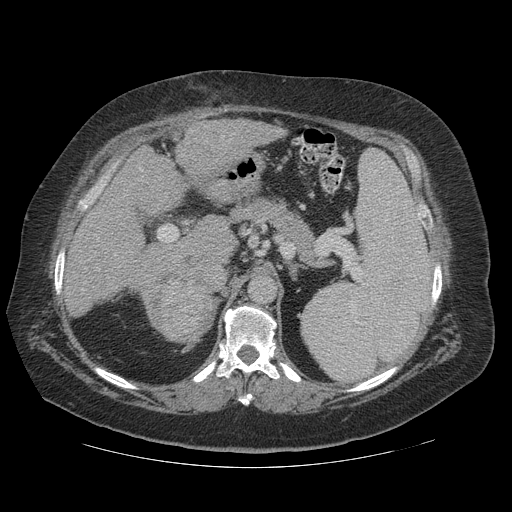
Contrast-enhanced abdominal CT (liver protocol), one axial slice. Slice 70 of 121 in the series (ordered by position). Soft-tissue window (W 400 / L 40 HU). 2.5 mm slice thickness. 512 × 512 image matrix, field of view 420 × 420 mm. From the clinical record (not read from this slice): diagnosis: hepatocellular carcinoma (patient treated with transarterial chemoembolisation; whether this scan precedes or follows treatment is not stated here); TNM stage (as recorded): Stage-IIIA; Child-Pugh class: A; tumour nodularity: multinodular; tumour size: 7.4 cm.
Annotated regions visible in this slice (semi-automatic segmentation, software-assisted and operator-edited):
- liver parenchyma outside the tumour (the mass and vessels are separate outlines, so this box may not span the whole liver): box from (x=64, y=120) to (x=286, y=320) px
- mass: (x=144, y=259)–(x=215, y=342)
- liver vessels: (x=82, y=133)–(x=234, y=291)